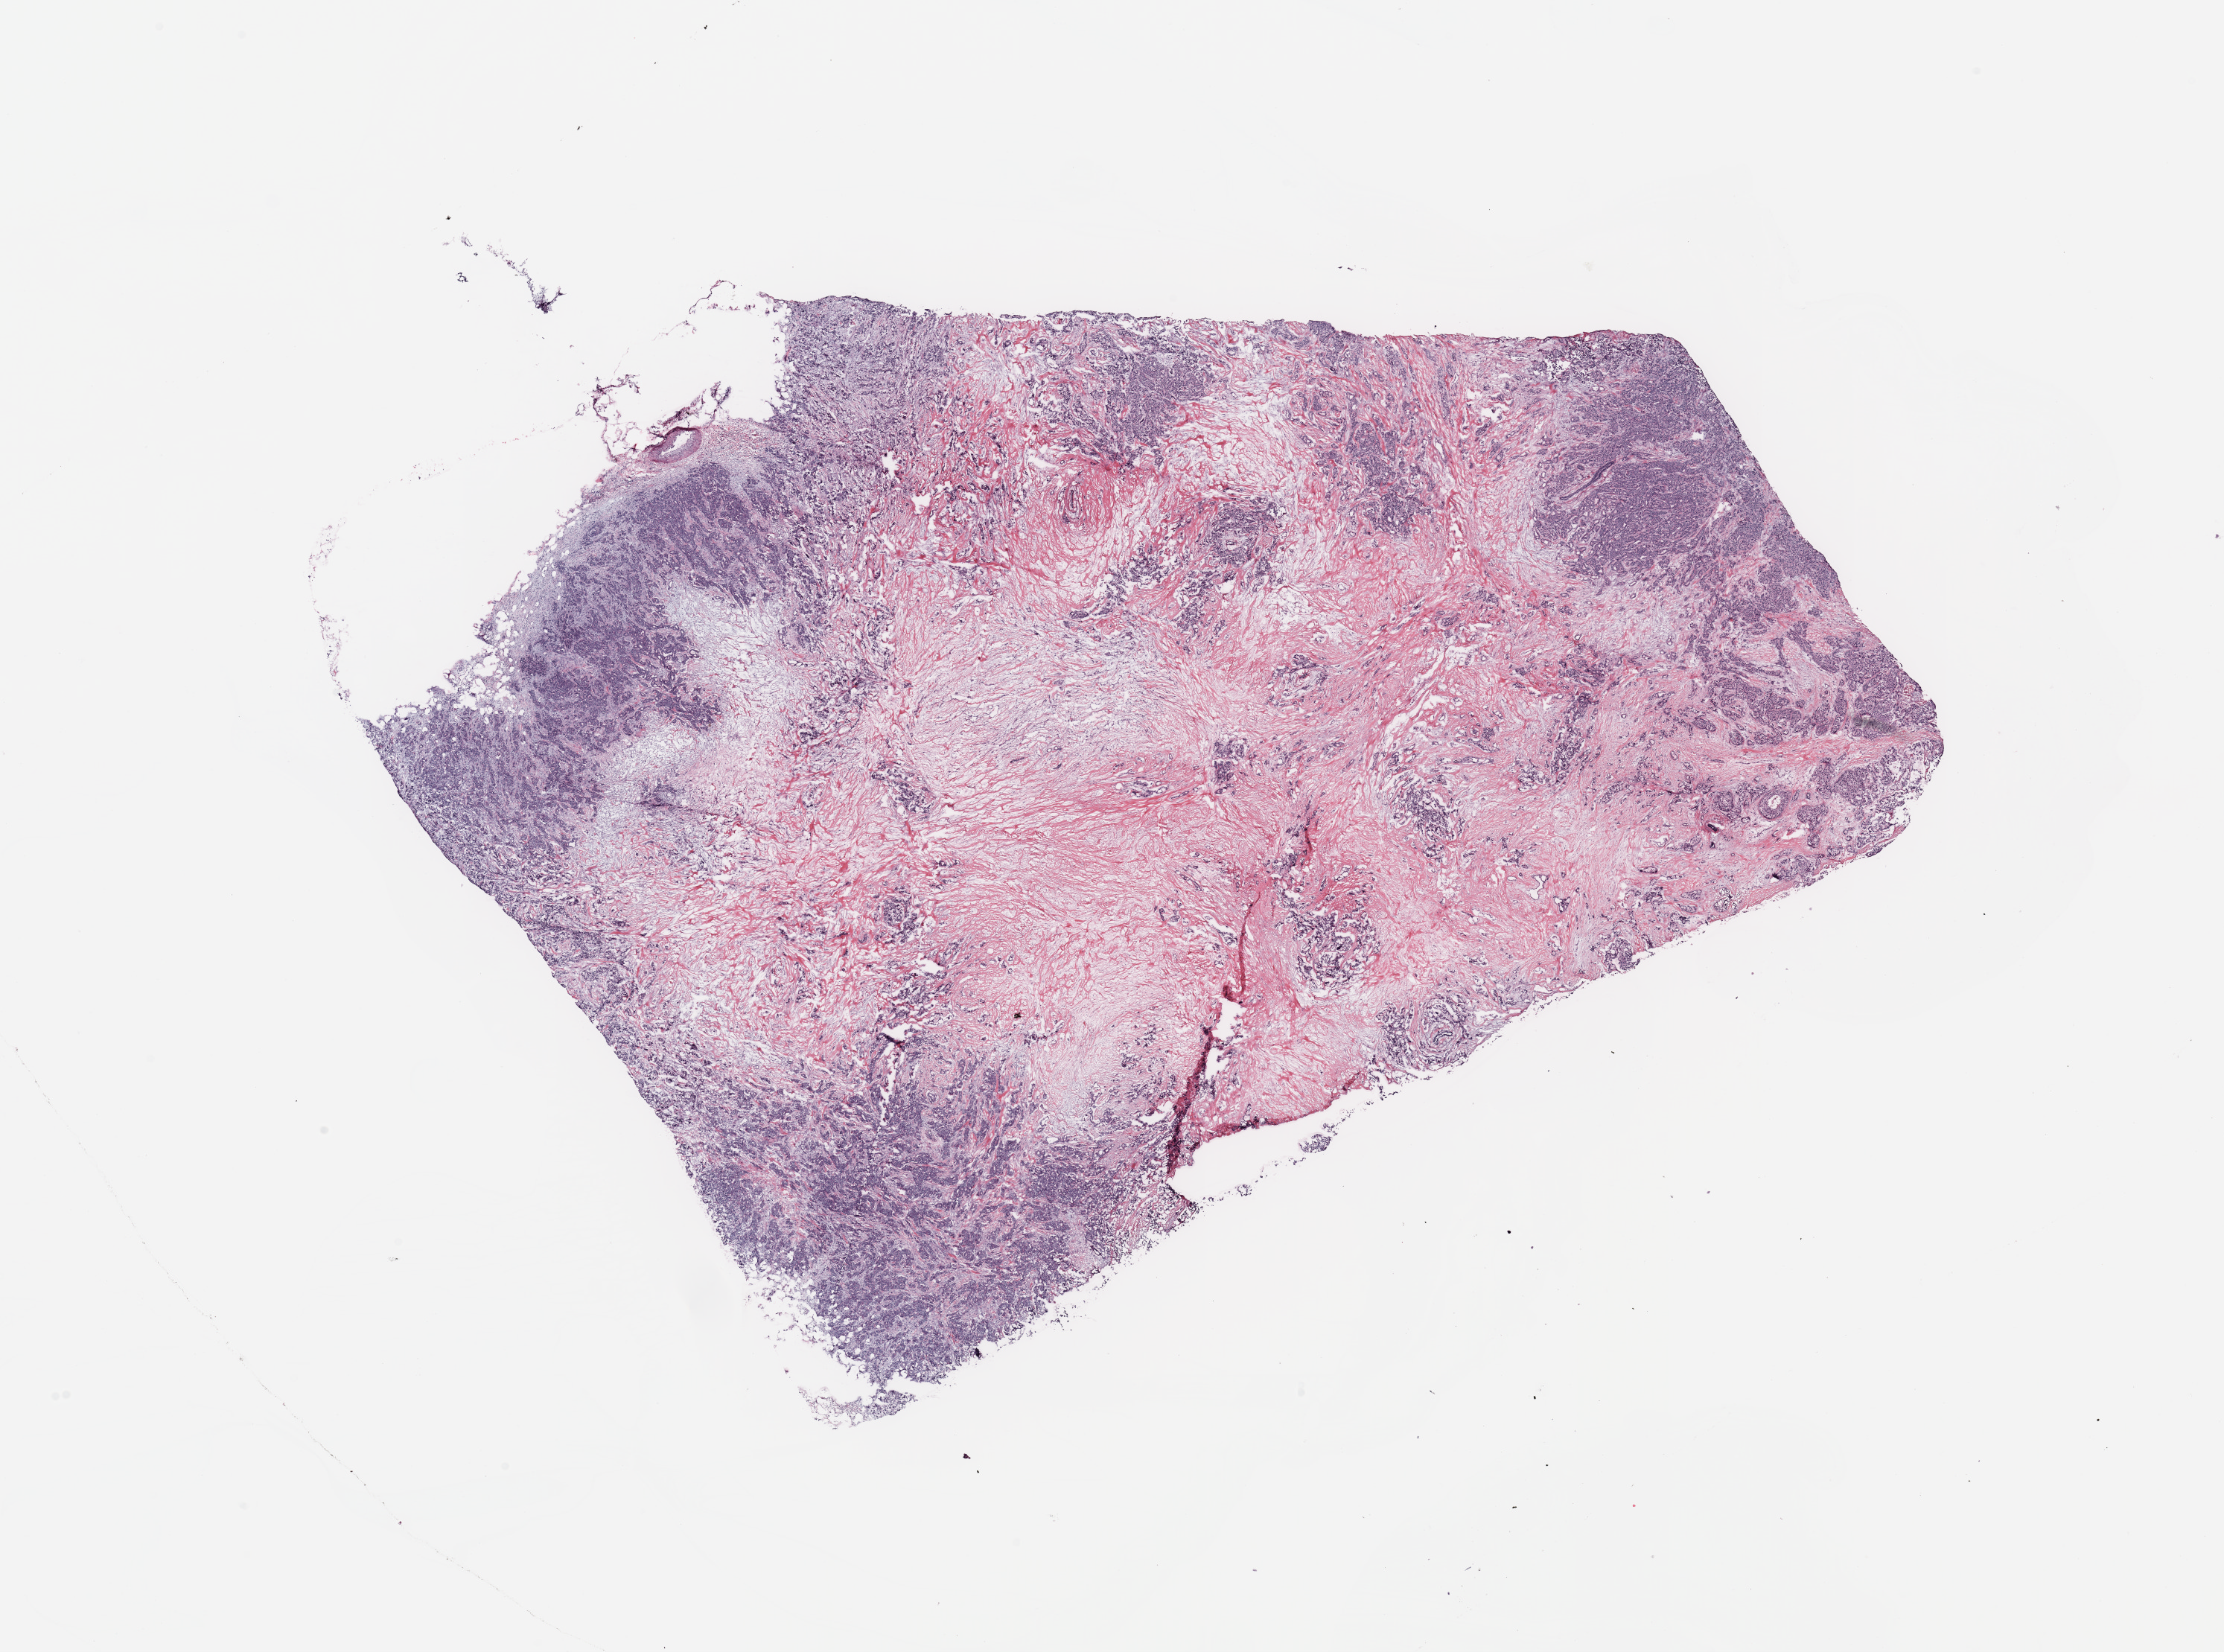
Hematoxylin and eosin (H&E) stained whole-slide image — whole scanned area (about 23.6 x 17.6 mm) shown as a low-resolution overview. Breast, tissue type not recorded.
Patient diagnosis (cohort enrolment): breast cancer (breast).